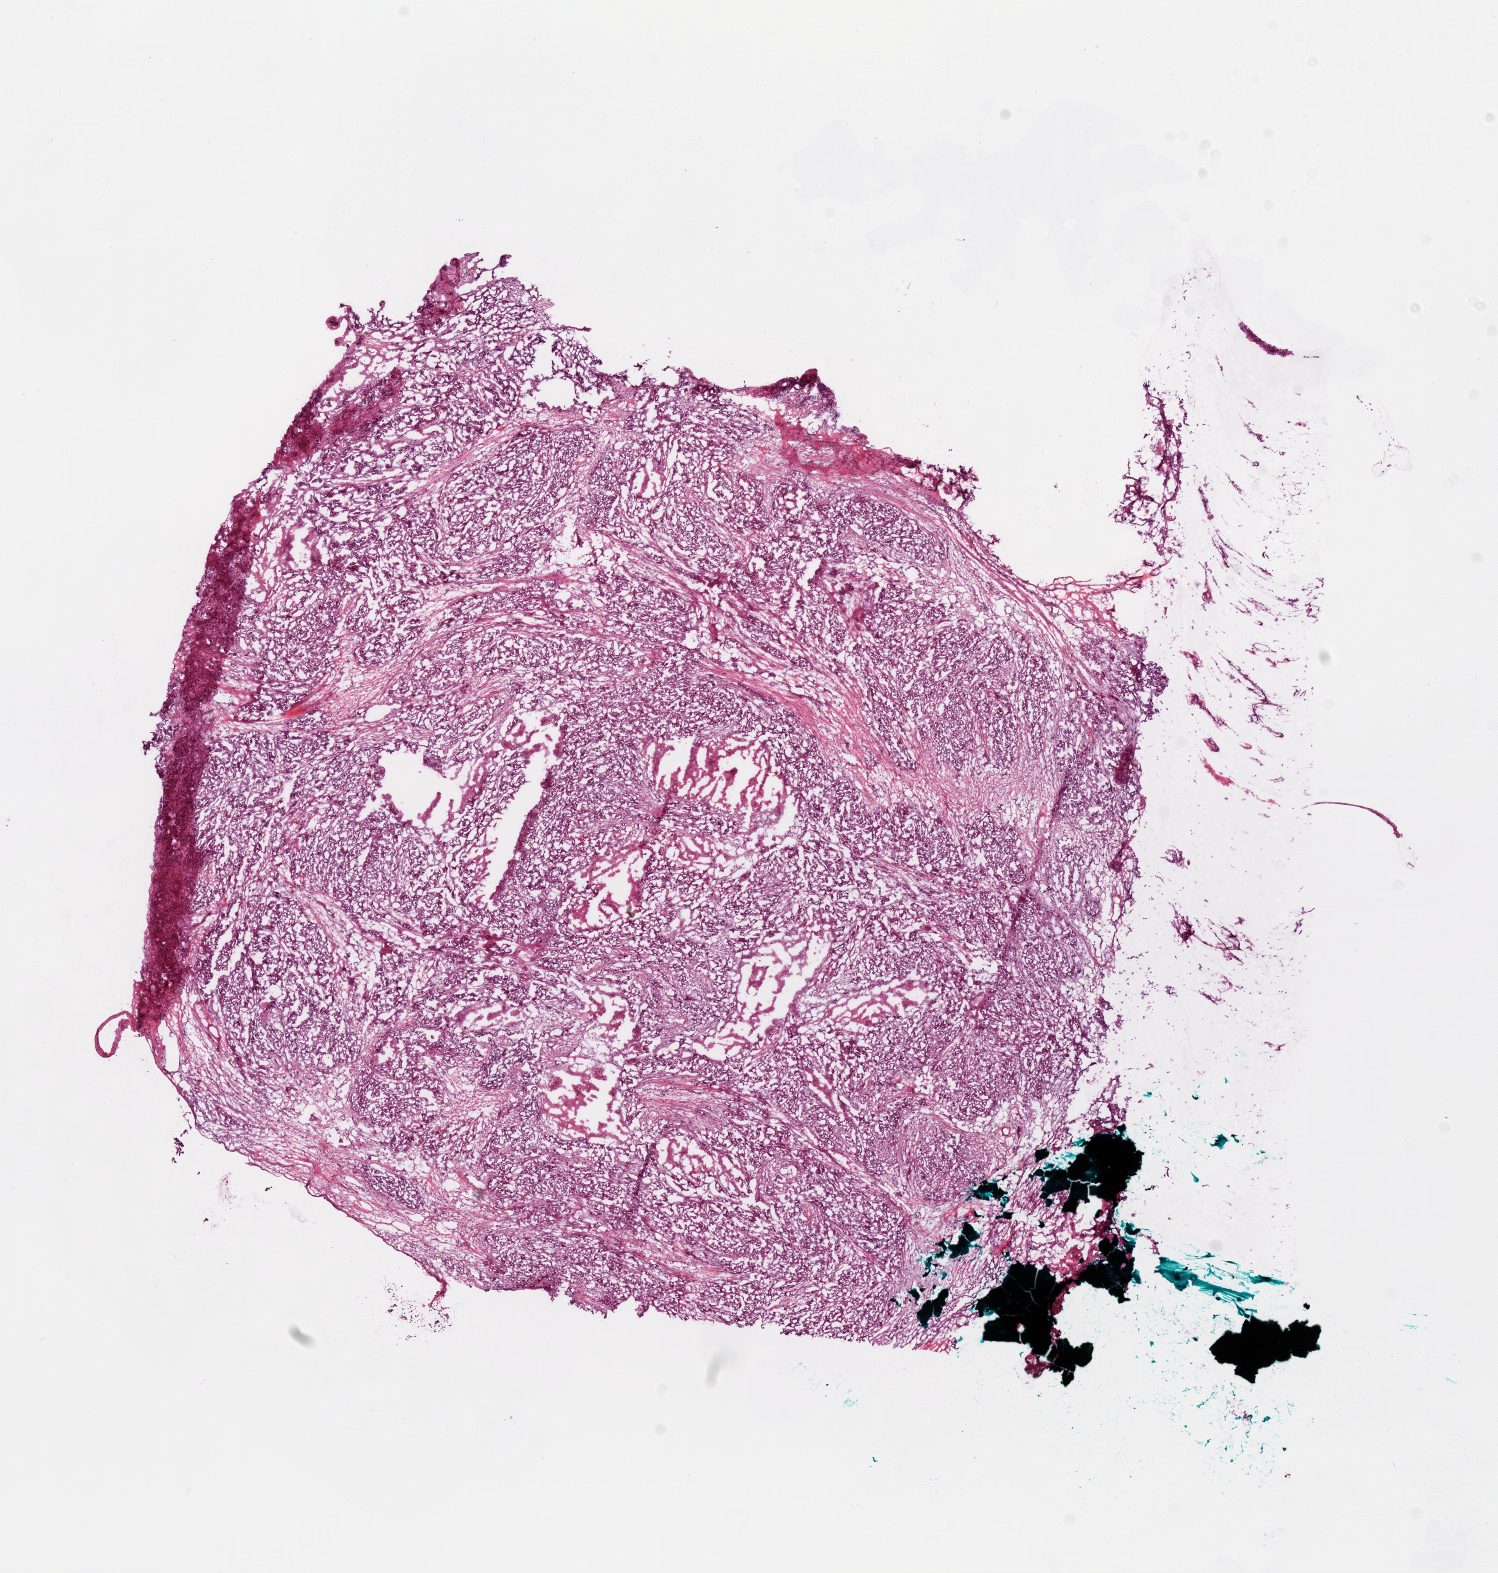
Digitized H&E-stained tissue section (whole slide), whole scanned area (about 12.1 x 12.7 mm, acquisition: 20x scan) shown as a low-resolution overview. Frozen section. Primary tumour sample from the ovary. Patient: female, age at initial diagnosis 58 years. Histologic grade: G3 (poorly differentiated). Composition of this section per pathologist review: tumour cells 80%, tumour nuclei 85%, normal cells 0%, stromal cells 15%, necrosis 5%.
* laterality: bilateral
* histologic diagnosis: Serous cystadenocarcinoma, NOS
* FIGO stage: IIIC